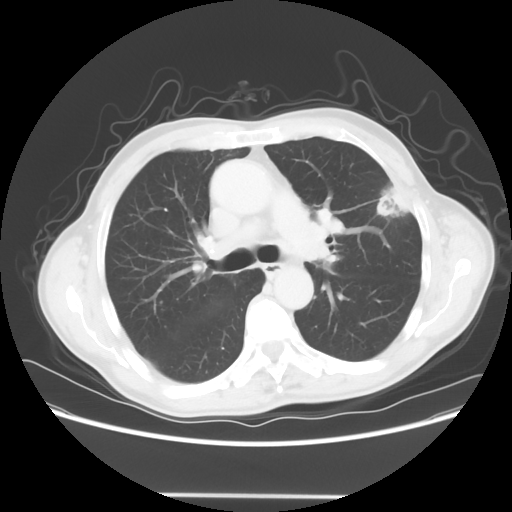
Chest CT, one axial slice; position 40 of 64 along the scan axis; lung window (W 1500 / L -600 HU); 5 mm slice thickness; 512 × 512 image matrix, field of view 392 × 392 mm. Male patient, age 71 years. Case-level facts recorded for this patient, not image findings: clinical TNM (as recorded): T1c N0 M0; histopathological grade: G2-3.
Outlined on this slice (rectangle marked by the reading radiologist):
- lung tumour (recorded histology: adenocarcinoma): bounding box <370,175,416,235> (left, top, right, bottom; pixels)